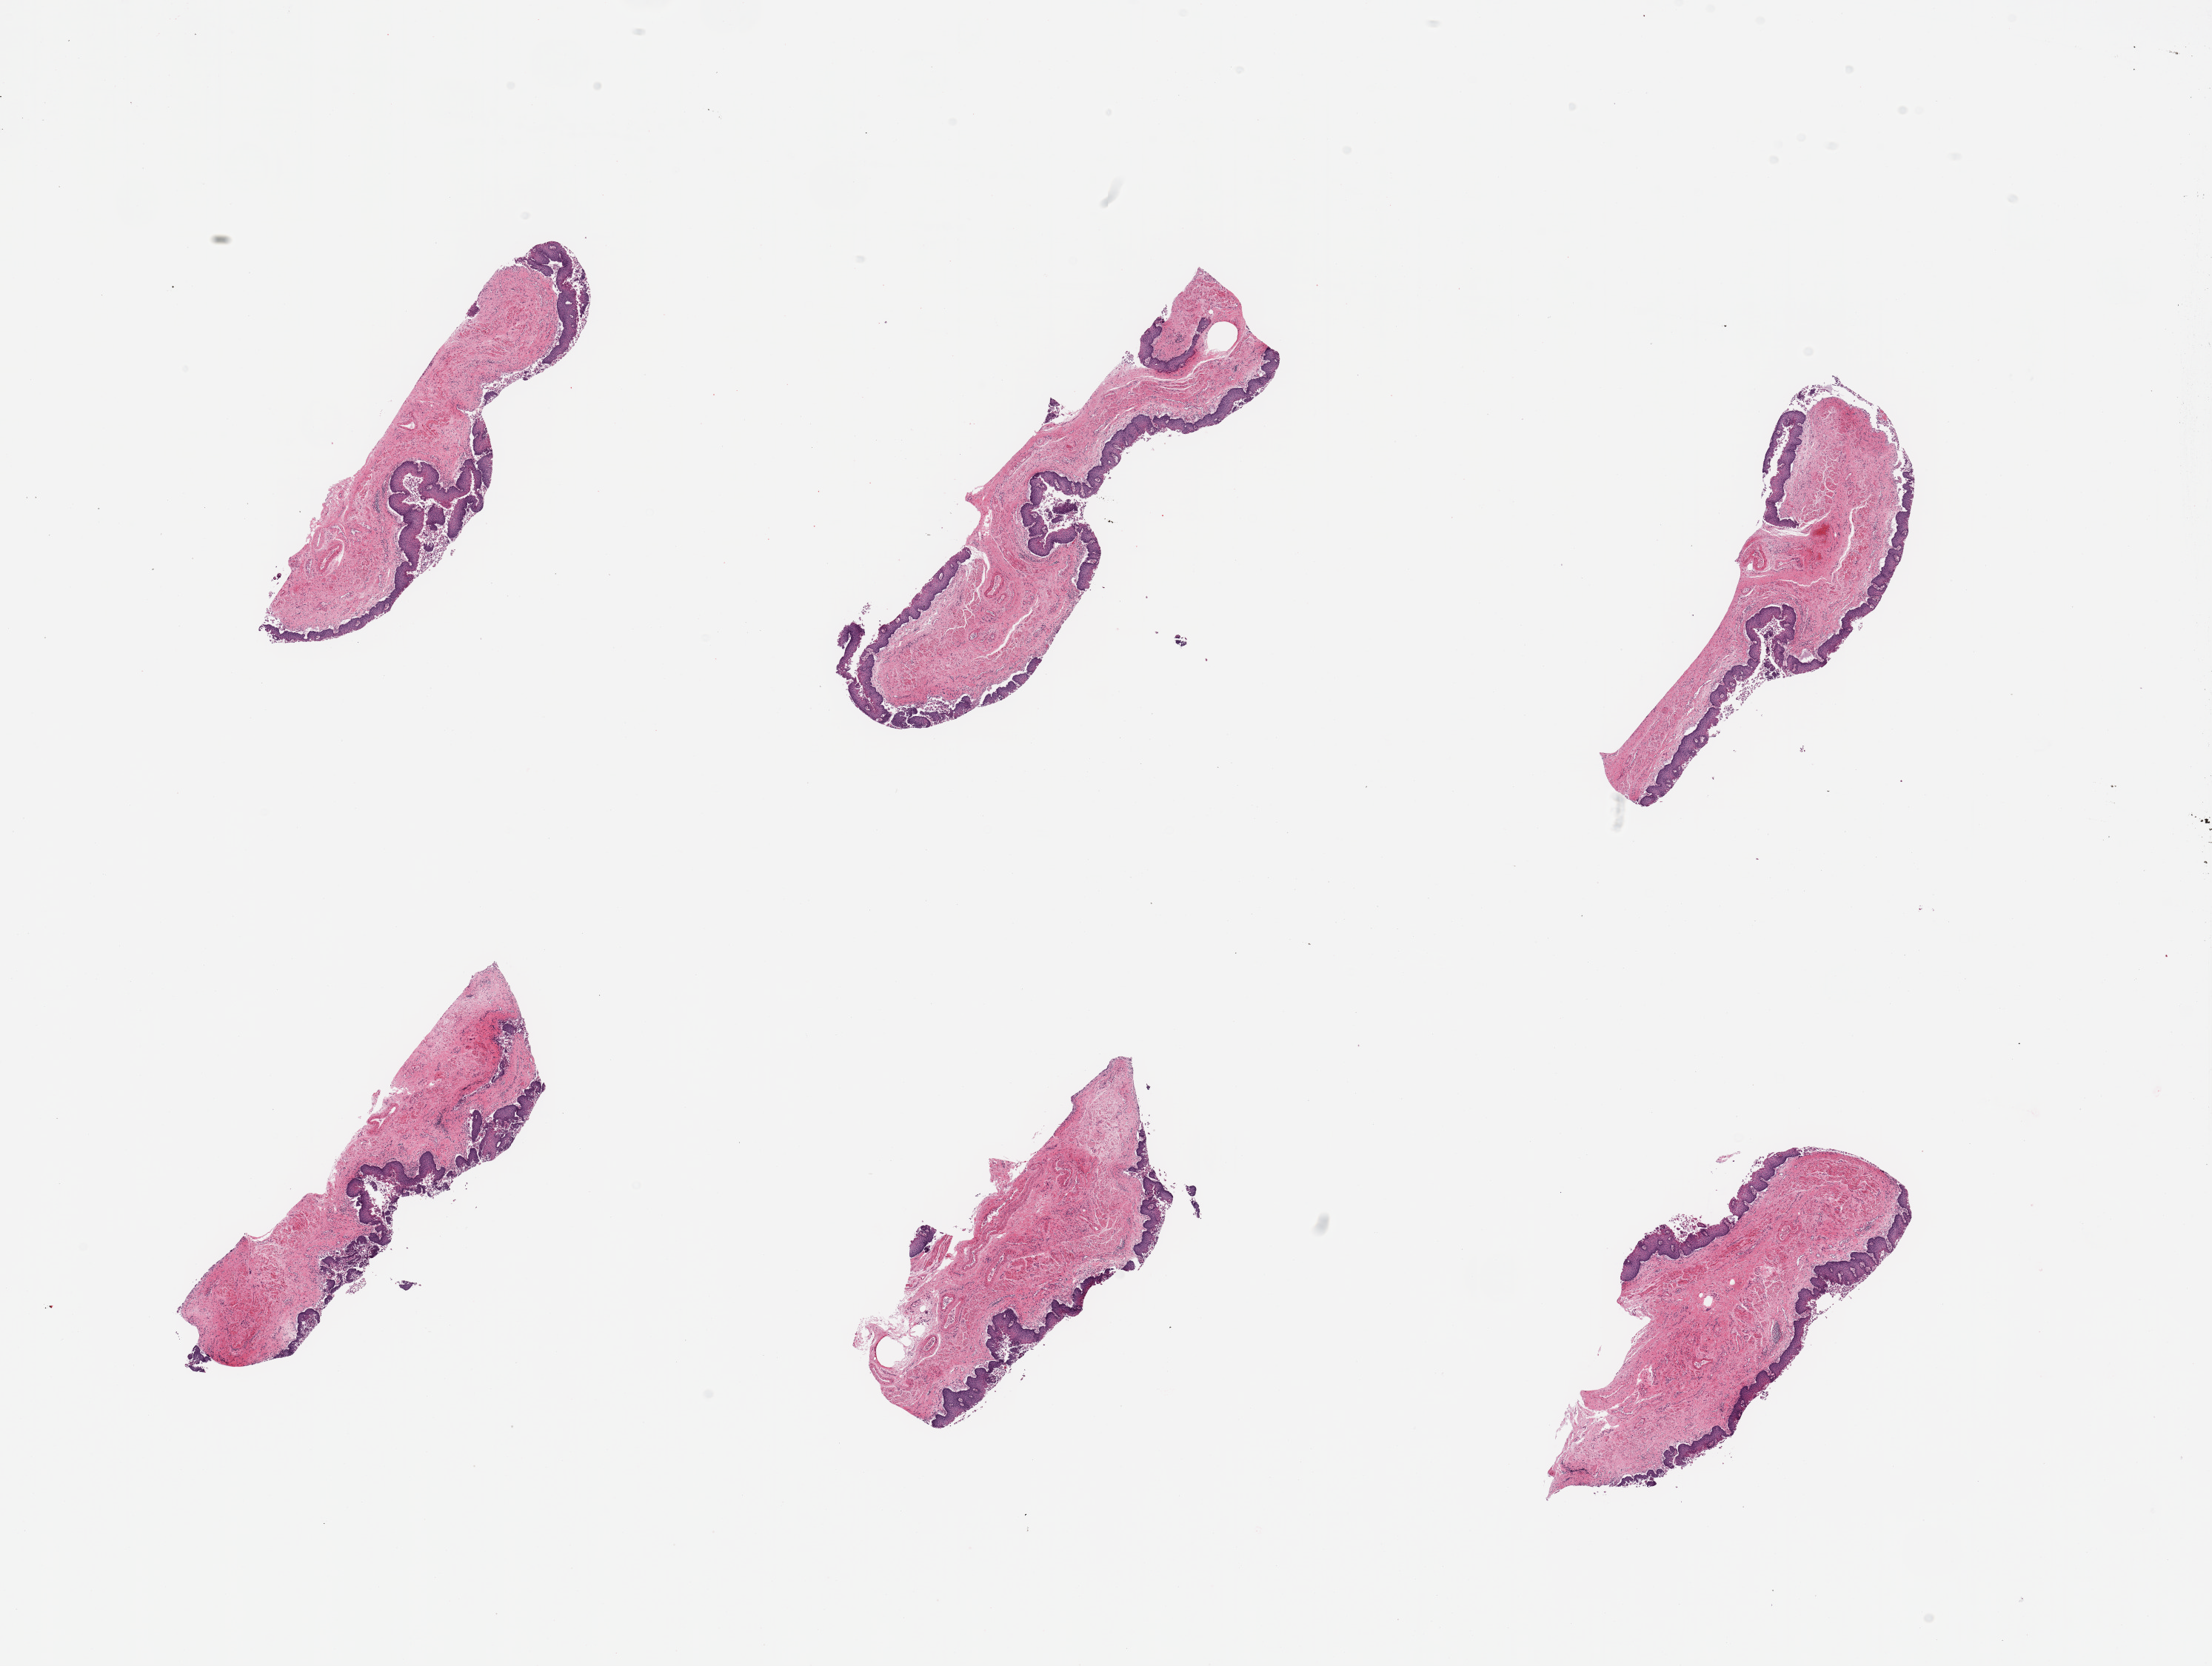
Whole-slide image, H&E stain, a low-resolution overview of the entire scanned area, about 23.6 x 17.8 mm, PAXgene-fixed paraffin-embedded (PFPE) section, section of esophageal mucous membrane (target tissue), tissue donor sample. Donor sex: female.
- pathologist's review note for this sample: 6 pieces, squamous mucosa up to ~ 0.25mm, early sloughing